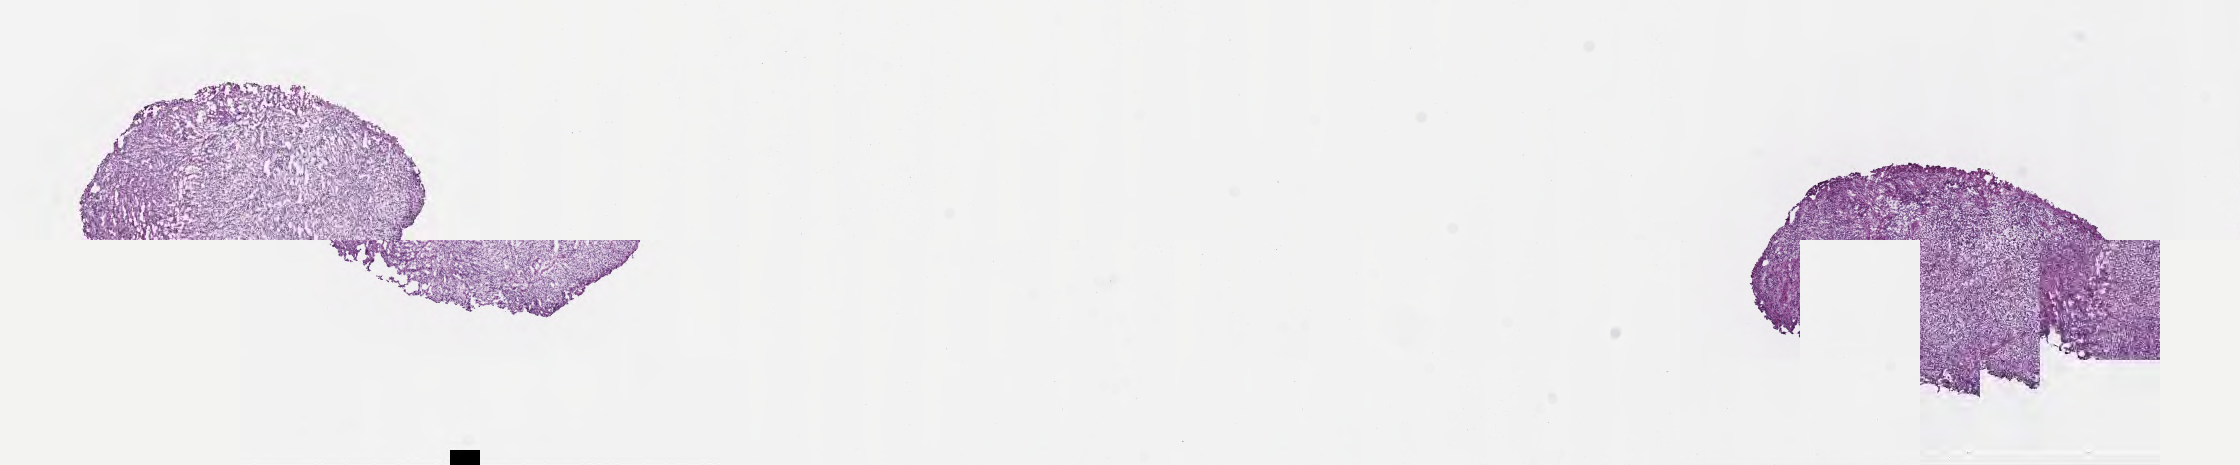
Digitized haematoxylin and eosin-stained section — low-resolution overview of the scanned area, about 18.1 x 3.8 mm. Cryosection. Specimen: primary tumor. Anatomic site: brain. Patient: female, age at initial diagnosis 49 years. Pathologist review of this section (percent, as recorded): tumor cells 86%, tumor nuclei 89%, stromal cells 2%, necrosis 1%, normal cells 11%. Infiltration values recorded for this section: lymphocyte infiltration 0%, monocyte infiltration 0%, neutrophil infiltration 0%.
Diagnosis: Glioblastoma, NOS.